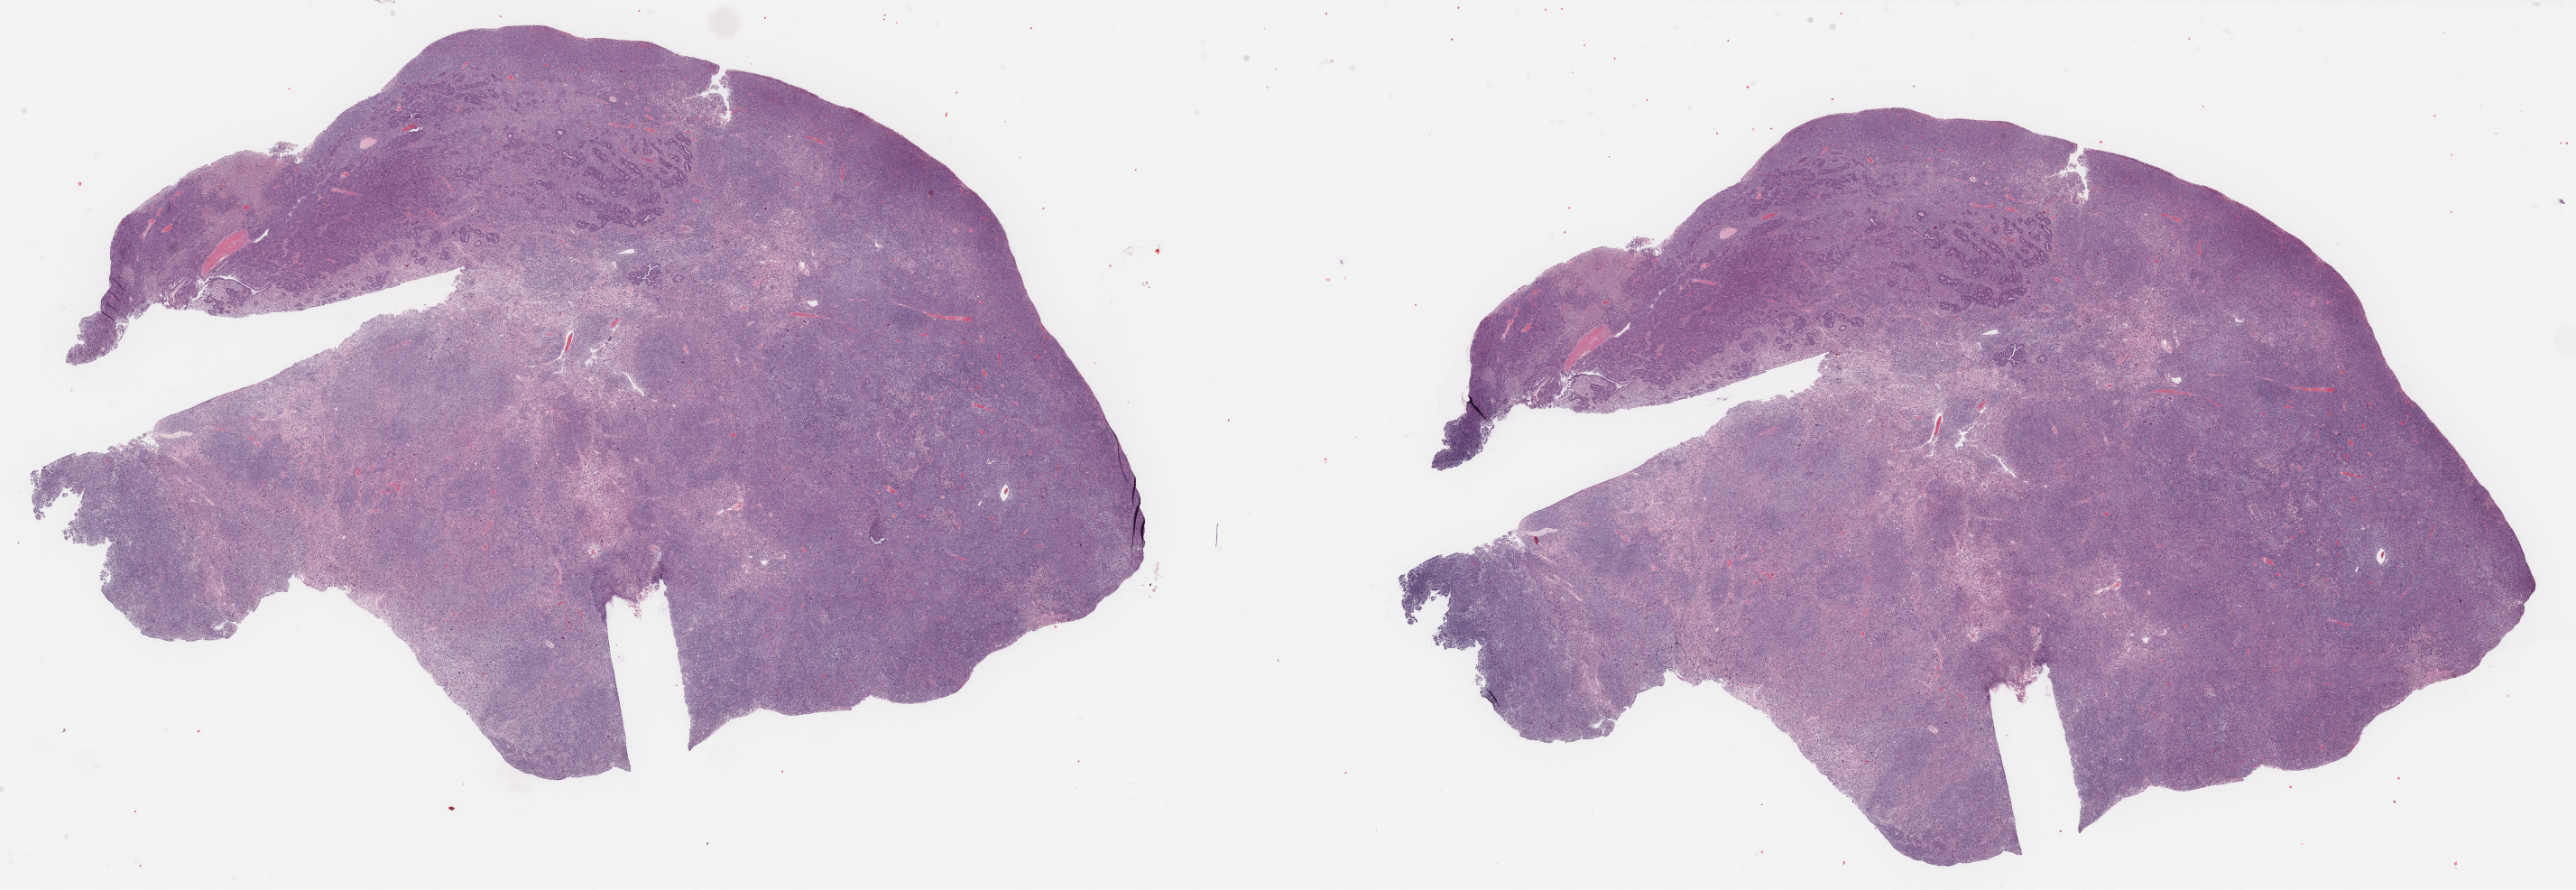
Digitized H&E tissue section (whole slide) — whole scanned area (about 45.2 x 15.6 mm, slide scanned at 40x) shown as a low-resolution overview. Formalin-fixed paraffin-embedded (FFPE) diagnostic section. Uterus, primary tumour sample. Patient sex: female.
• FIGO stage: IIIC1
• histologic diagnosis: Carcinosarcoma, NOS